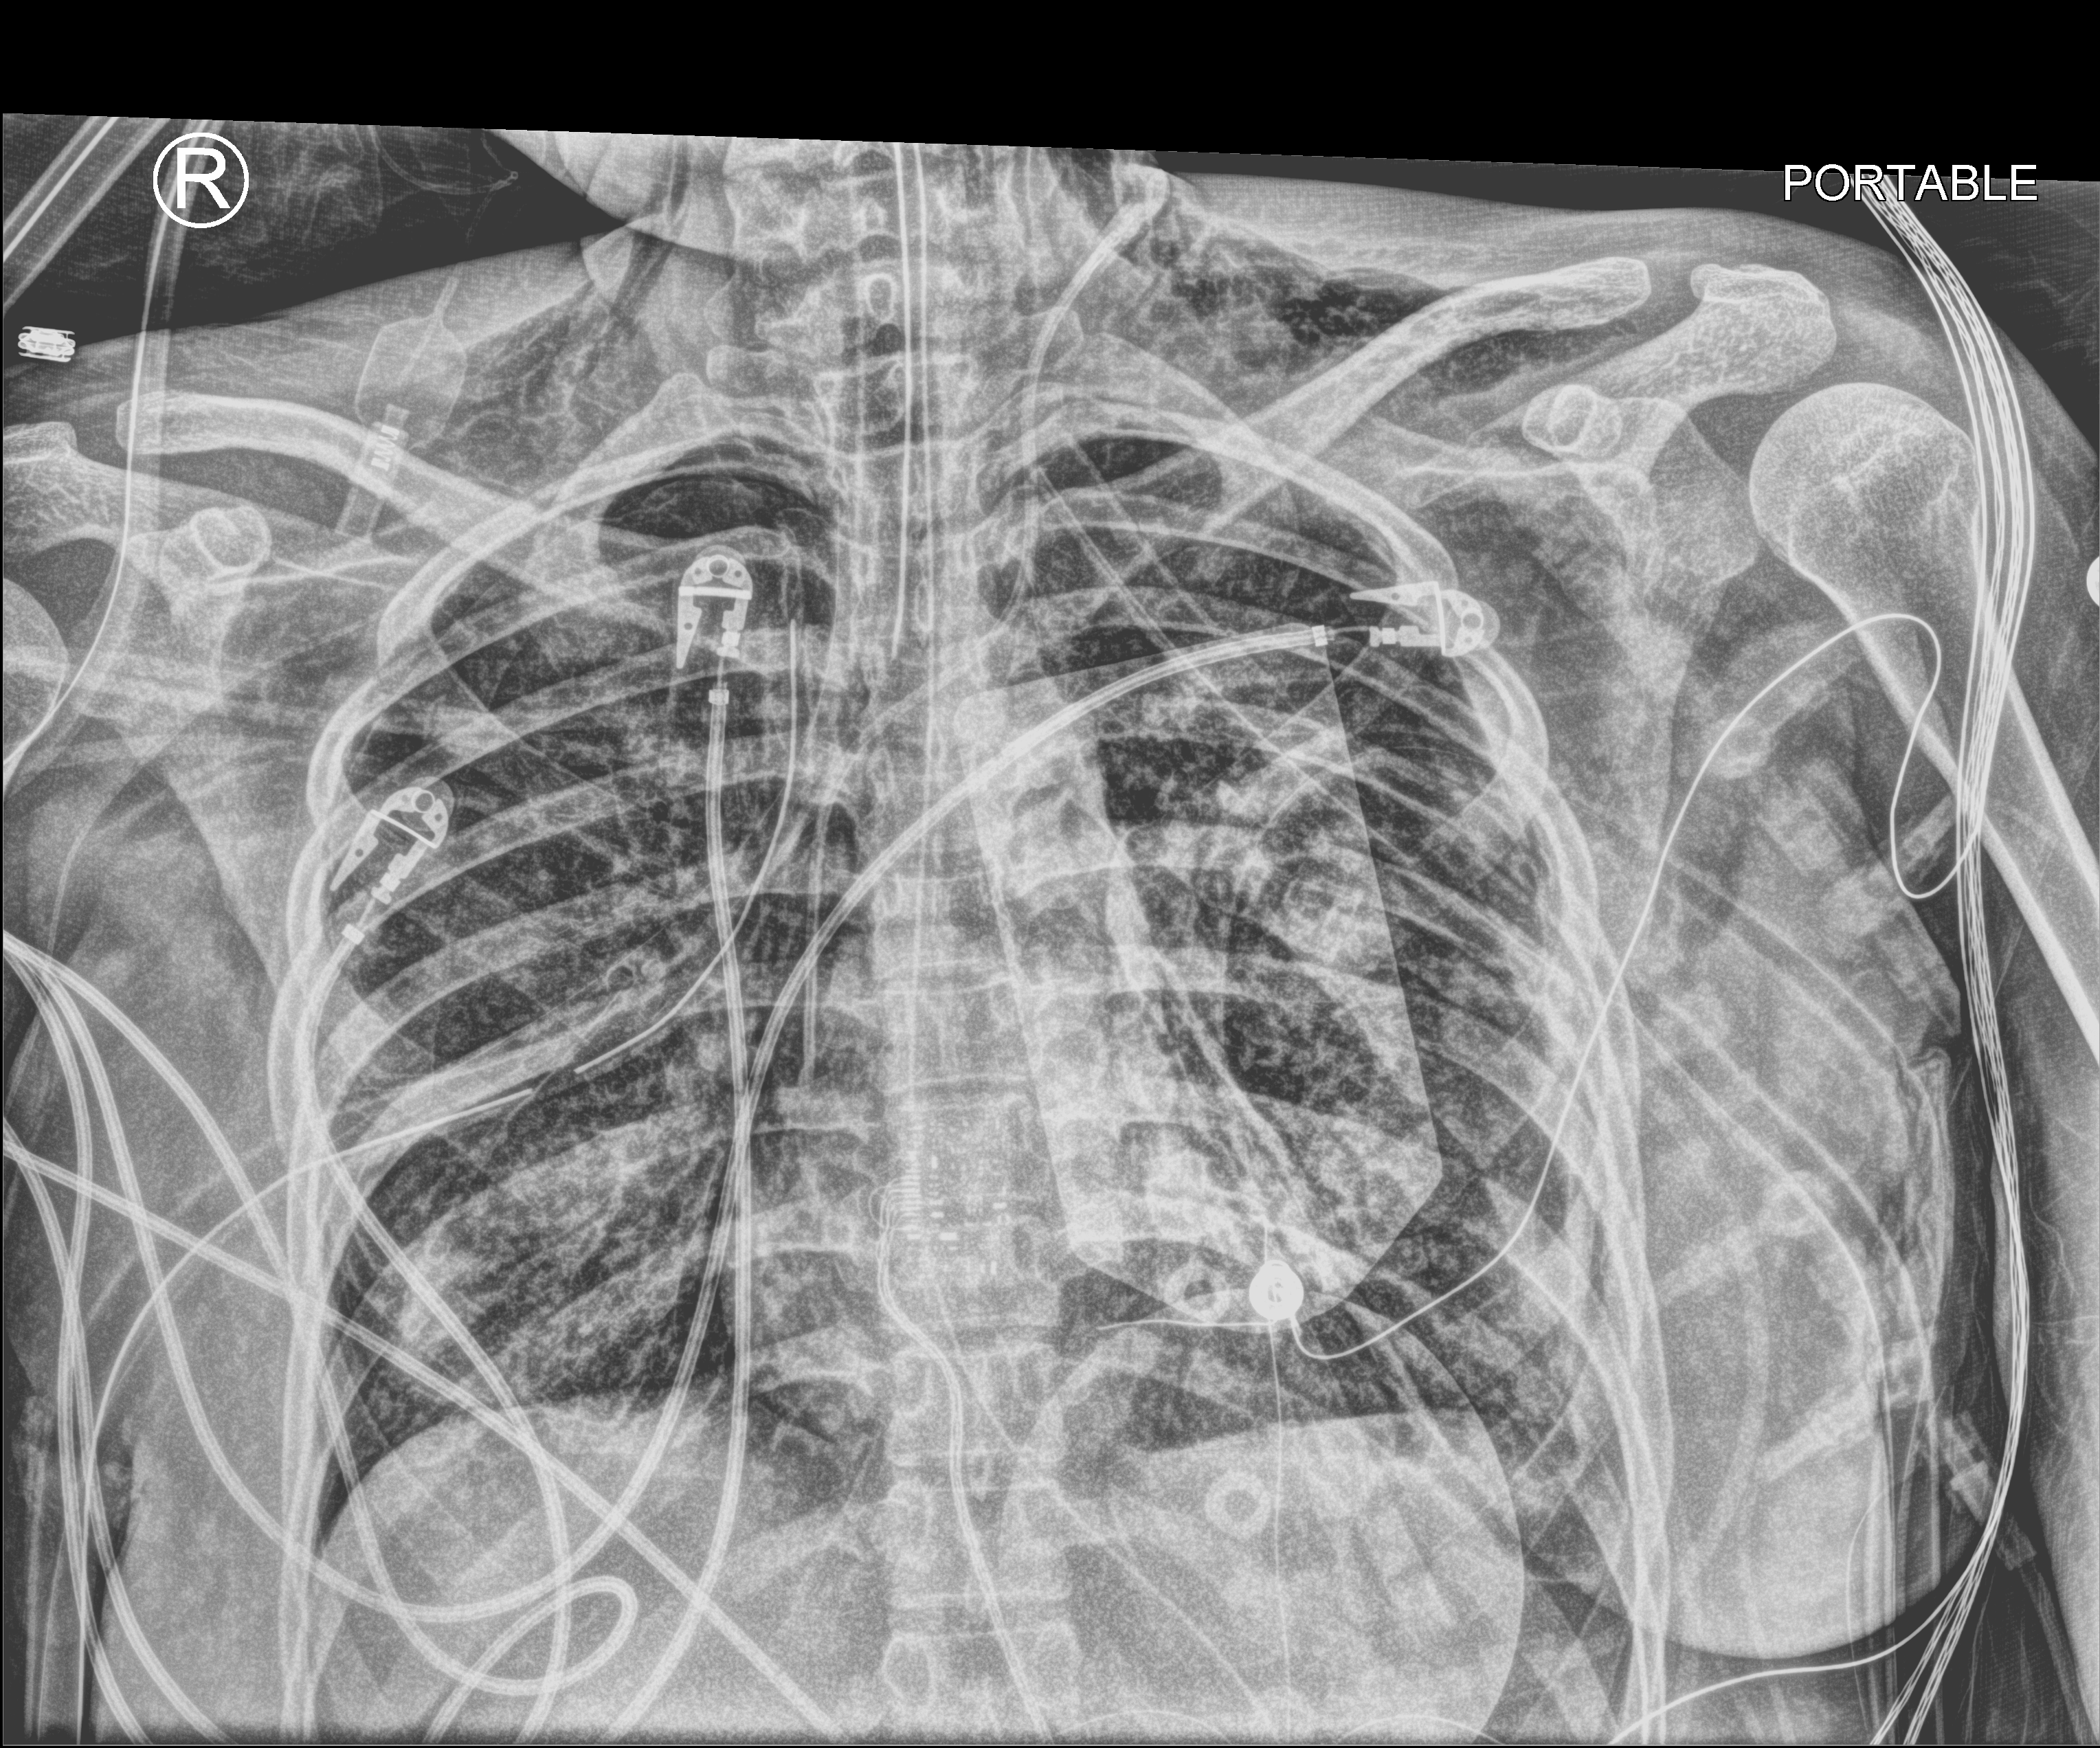
Chest X-ray (portable). Adult patient hospitalised with COVID-19, age 18–59 years.
Admission-level facts for this patient (not findings on this image; timing relative to this image not recorded):
- hypertension (admission record): no
- length of hospital stay: 30 days